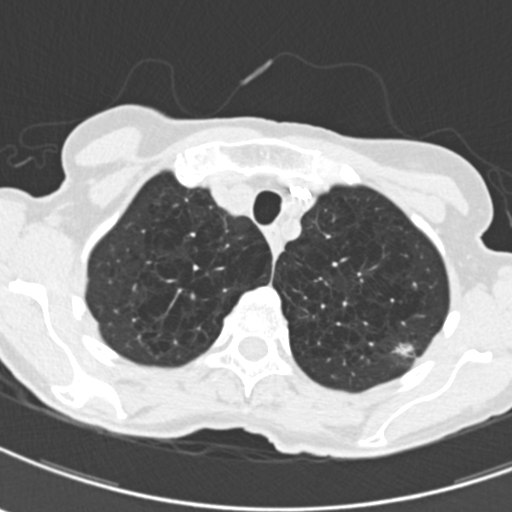
Low-dose screening chest CT, one axial slice. Position 167 of 203 along the scan axis. 120 kVp. Lung window (W 1500 / L -600 HU). 2 mm slice thickness. 512 × 512 image matrix, field of view 279 × 279 mm.
Outlined on this slice (expert manual segmentation):
- lesion 1 (tumor, upper lobe of left lung): bounding box (x1, y1, x2, y2) in pixels: (391, 342, 416, 358)